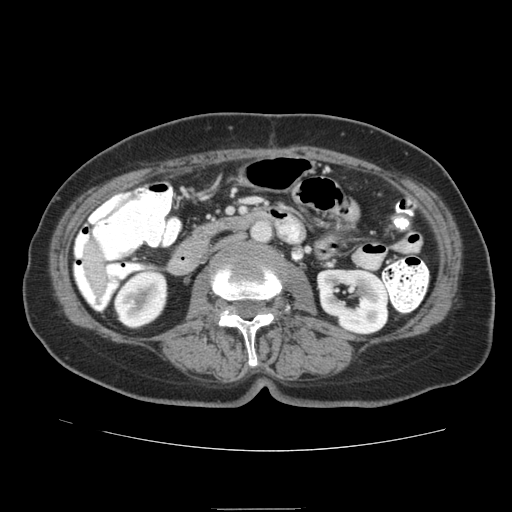
Contrast-enhanced abdominal CT (liver protocol), one axial slice. Slice 20 of 95 in the series (ordered by position). 140 kVp. Soft-tissue window (W 400 / L 40 HU). 2.5 mm slice thickness. 512 × 512 image matrix. From the clinical record (not read from this slice): diagnosis: hepatocellular carcinoma (patient treated with transarterial chemoembolisation; whether this scan precedes or follows treatment is not stated here); TNM stage (as recorded): Stage-IVA; Child-Pugh class: B; tumour differentiation: moderately differentiated.
Outlined on this slice (semi-automatically segmented with operator editing):
- liver parenchyma outside the tumour (the mass and vessels are separate outlines, so this box may not span the whole liver): bounding box <88,246,104,266> (left, top, right, bottom; pixels)